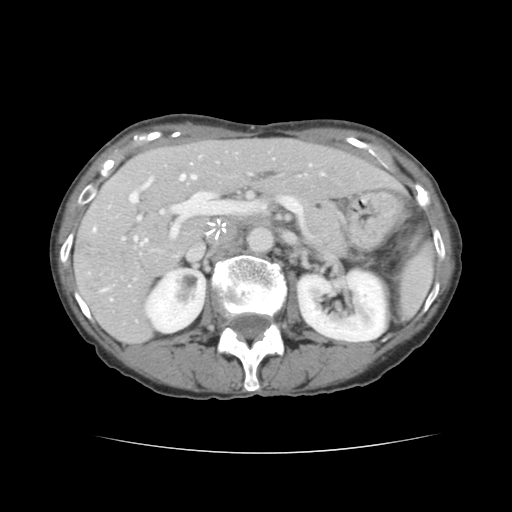
Contrast-enhanced abdominal CT, one axial slice. Slice 77 of 136 in the series (ordered by position). Soft-tissue window (W 400 / L 40 HU). 512 × 512 image matrix, field of view 319 × 319 mm. Female patient, age 77 years. Case-level facts recorded for this patient, not image findings: diagnosis: colorectal cancer liver metastases, imaged before liver resection; multiple liver metastases: yes; largest metastasis: 3 cm; disease in both lobes: no.
Outlined on this slice (manually delineated by an expert):
- hepatic veins: bounding box <134,174,323,240> (left, top, right, bottom; pixels)
- liver: <75,139,399,342>
- planned liver remnant (the part of the liver to remain after resection): <155,140,397,199>
- portal vein (with intrahepatic branches): <94,179,238,291>